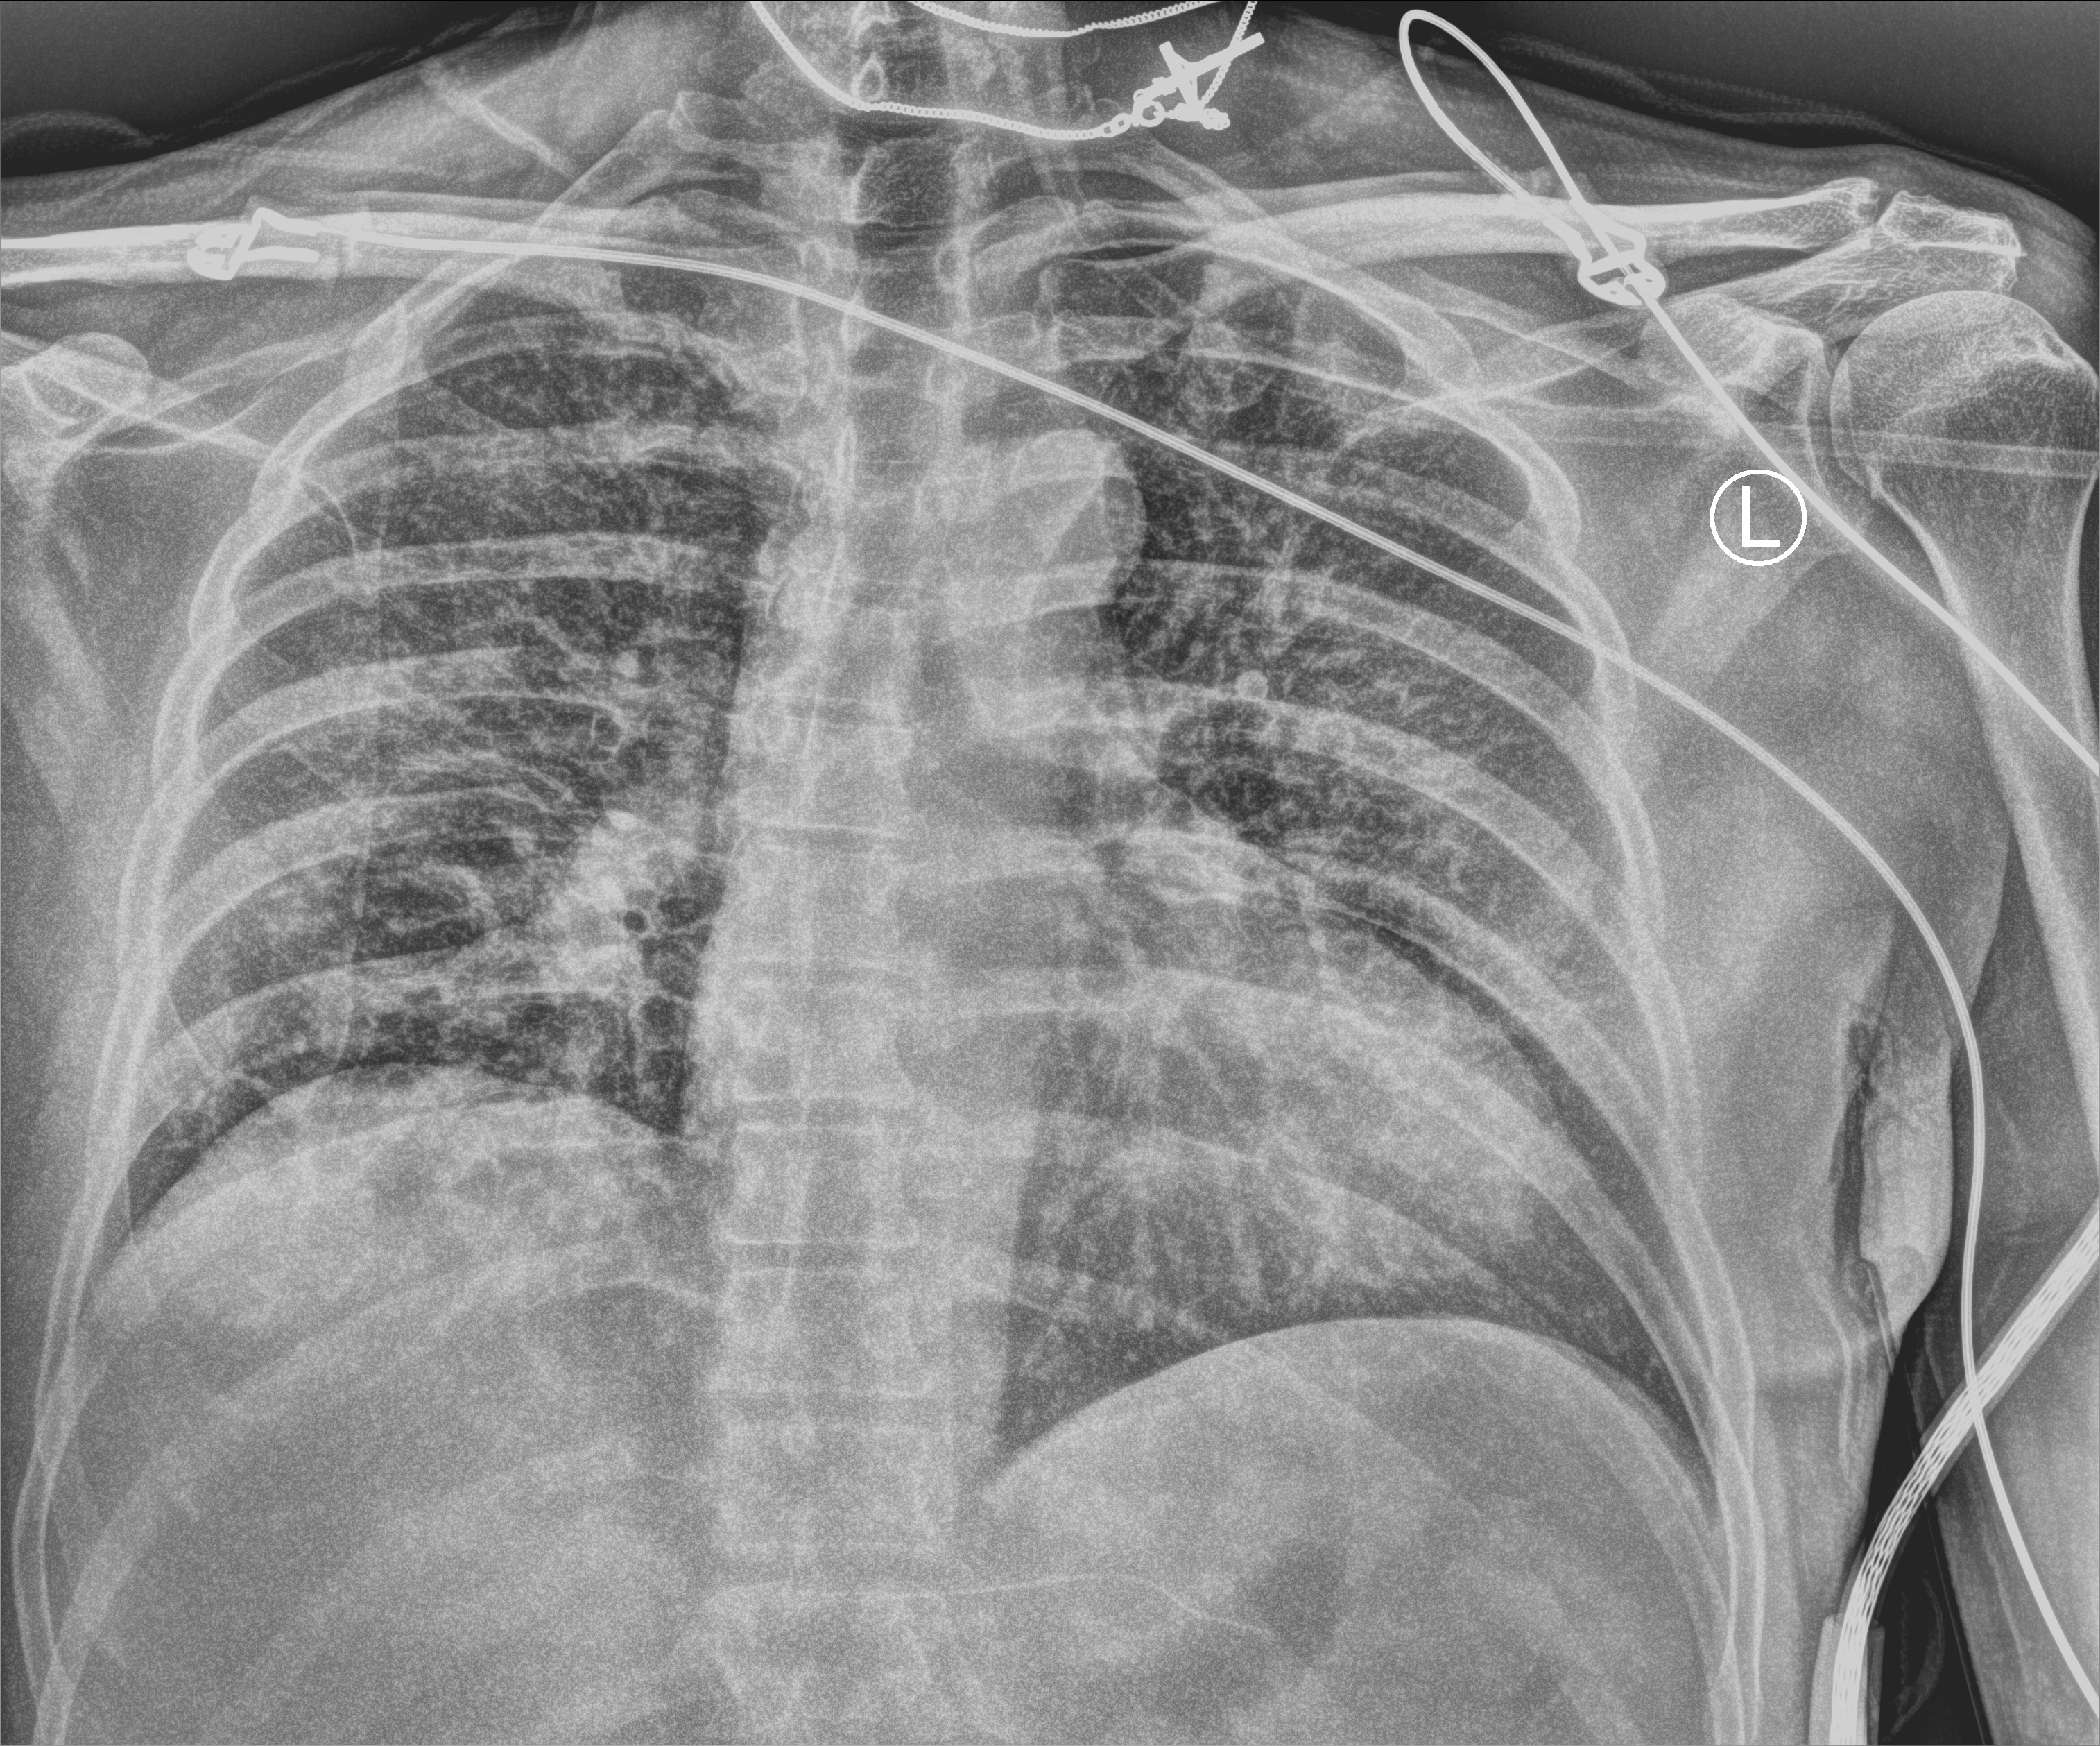
Chest X-ray (portable); anteroposterior (AP) projection. Male patient hospitalised with COVID-19, age 60–74 years.
Hospital-stay facts (about this admission, not read from this image; timing relative to this image not recorded):
- COPD (admission record): no
- admitted to intensive care during this hospital stay: no